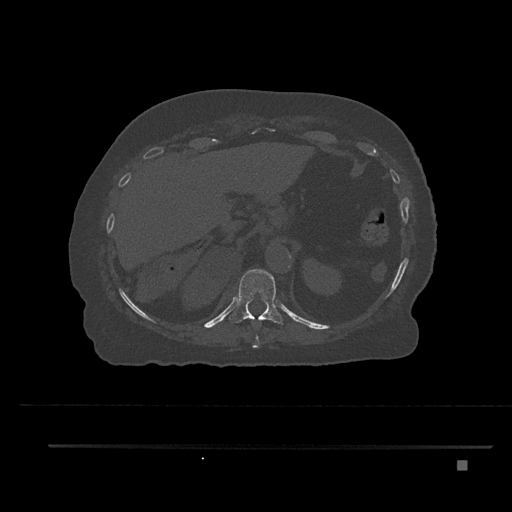
CT including the spine, one axial slice; position 317 of 797 along the scan axis; reconstruction kernel Br40s/3; bone window (W 1800 / L 400 HU); 512 × 512 image matrix, field of view 437 × 437 mm. Patient: female, 76 years. From the clinical record (not read from this slice): primary cancer: lung.
Outlined on this slice (semi-automatic segmentation, software-assisted and operator-edited):
- T10 vertebra: bounding box (x1, y1, x2, y2) in pixels: (253, 325, 260, 348)
- T11 vertebra: (229, 269, 284, 325)